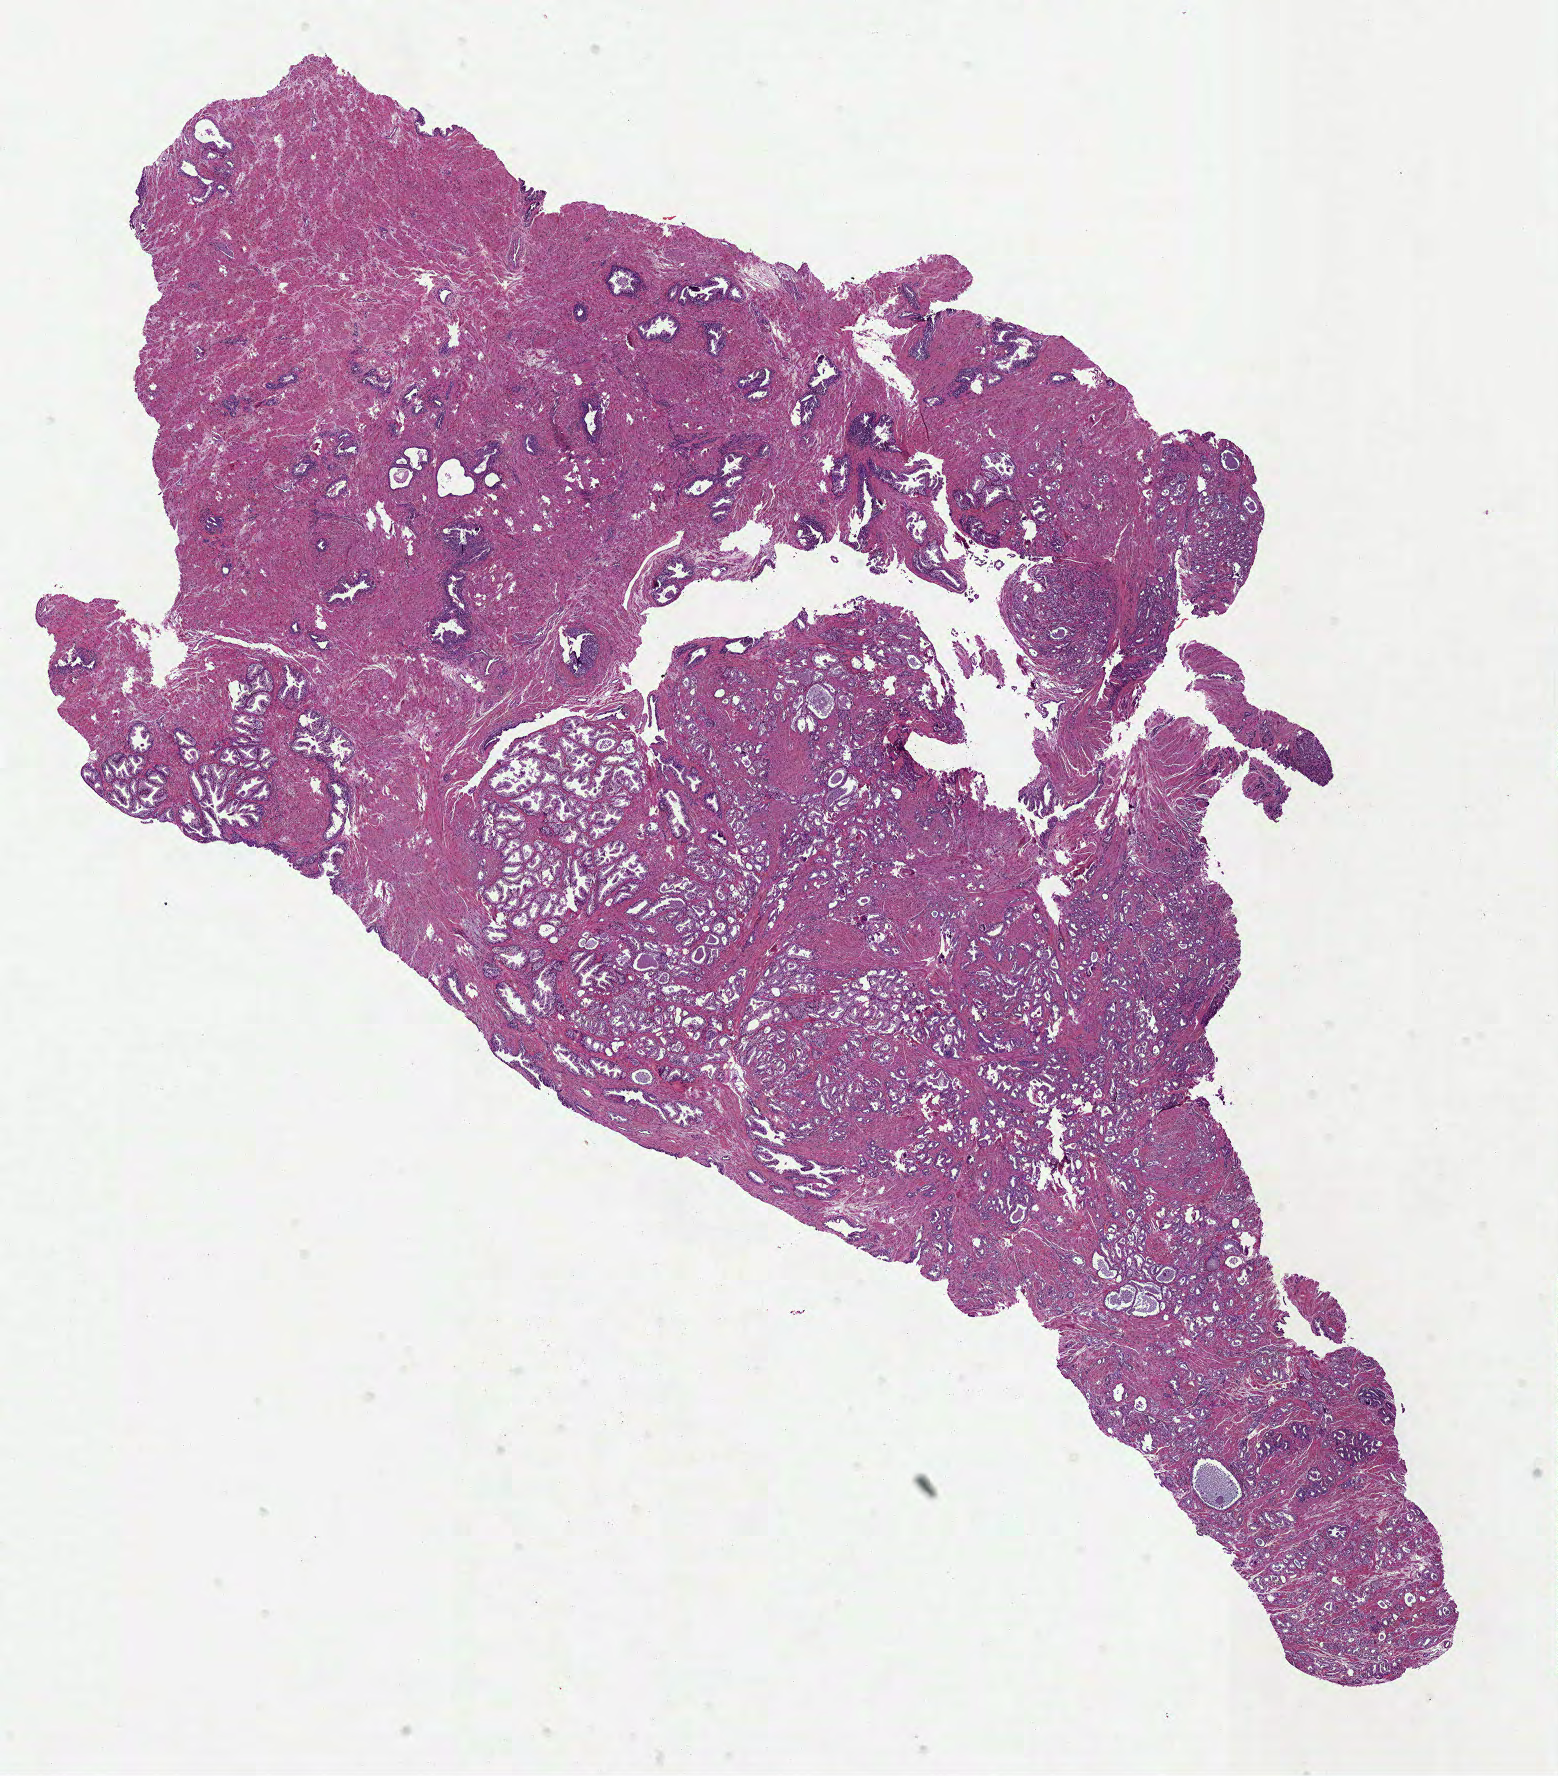
Digitized H&E-stained tissue section (whole slide), low-resolution overview of the scanned area, about 12.6 x 14.3 mm (slide scanned at 40x), FFPE section, prostate, primary tumour sample. Patient: male, age at initial diagnosis 59 years. Gleason score: 7 (3+4).
Histologic diagnosis: Acinar cell carcinoma (prostate gland). Lymph nodes positive (case pathology): 0 of 4 examined. Laterality: bilateral.